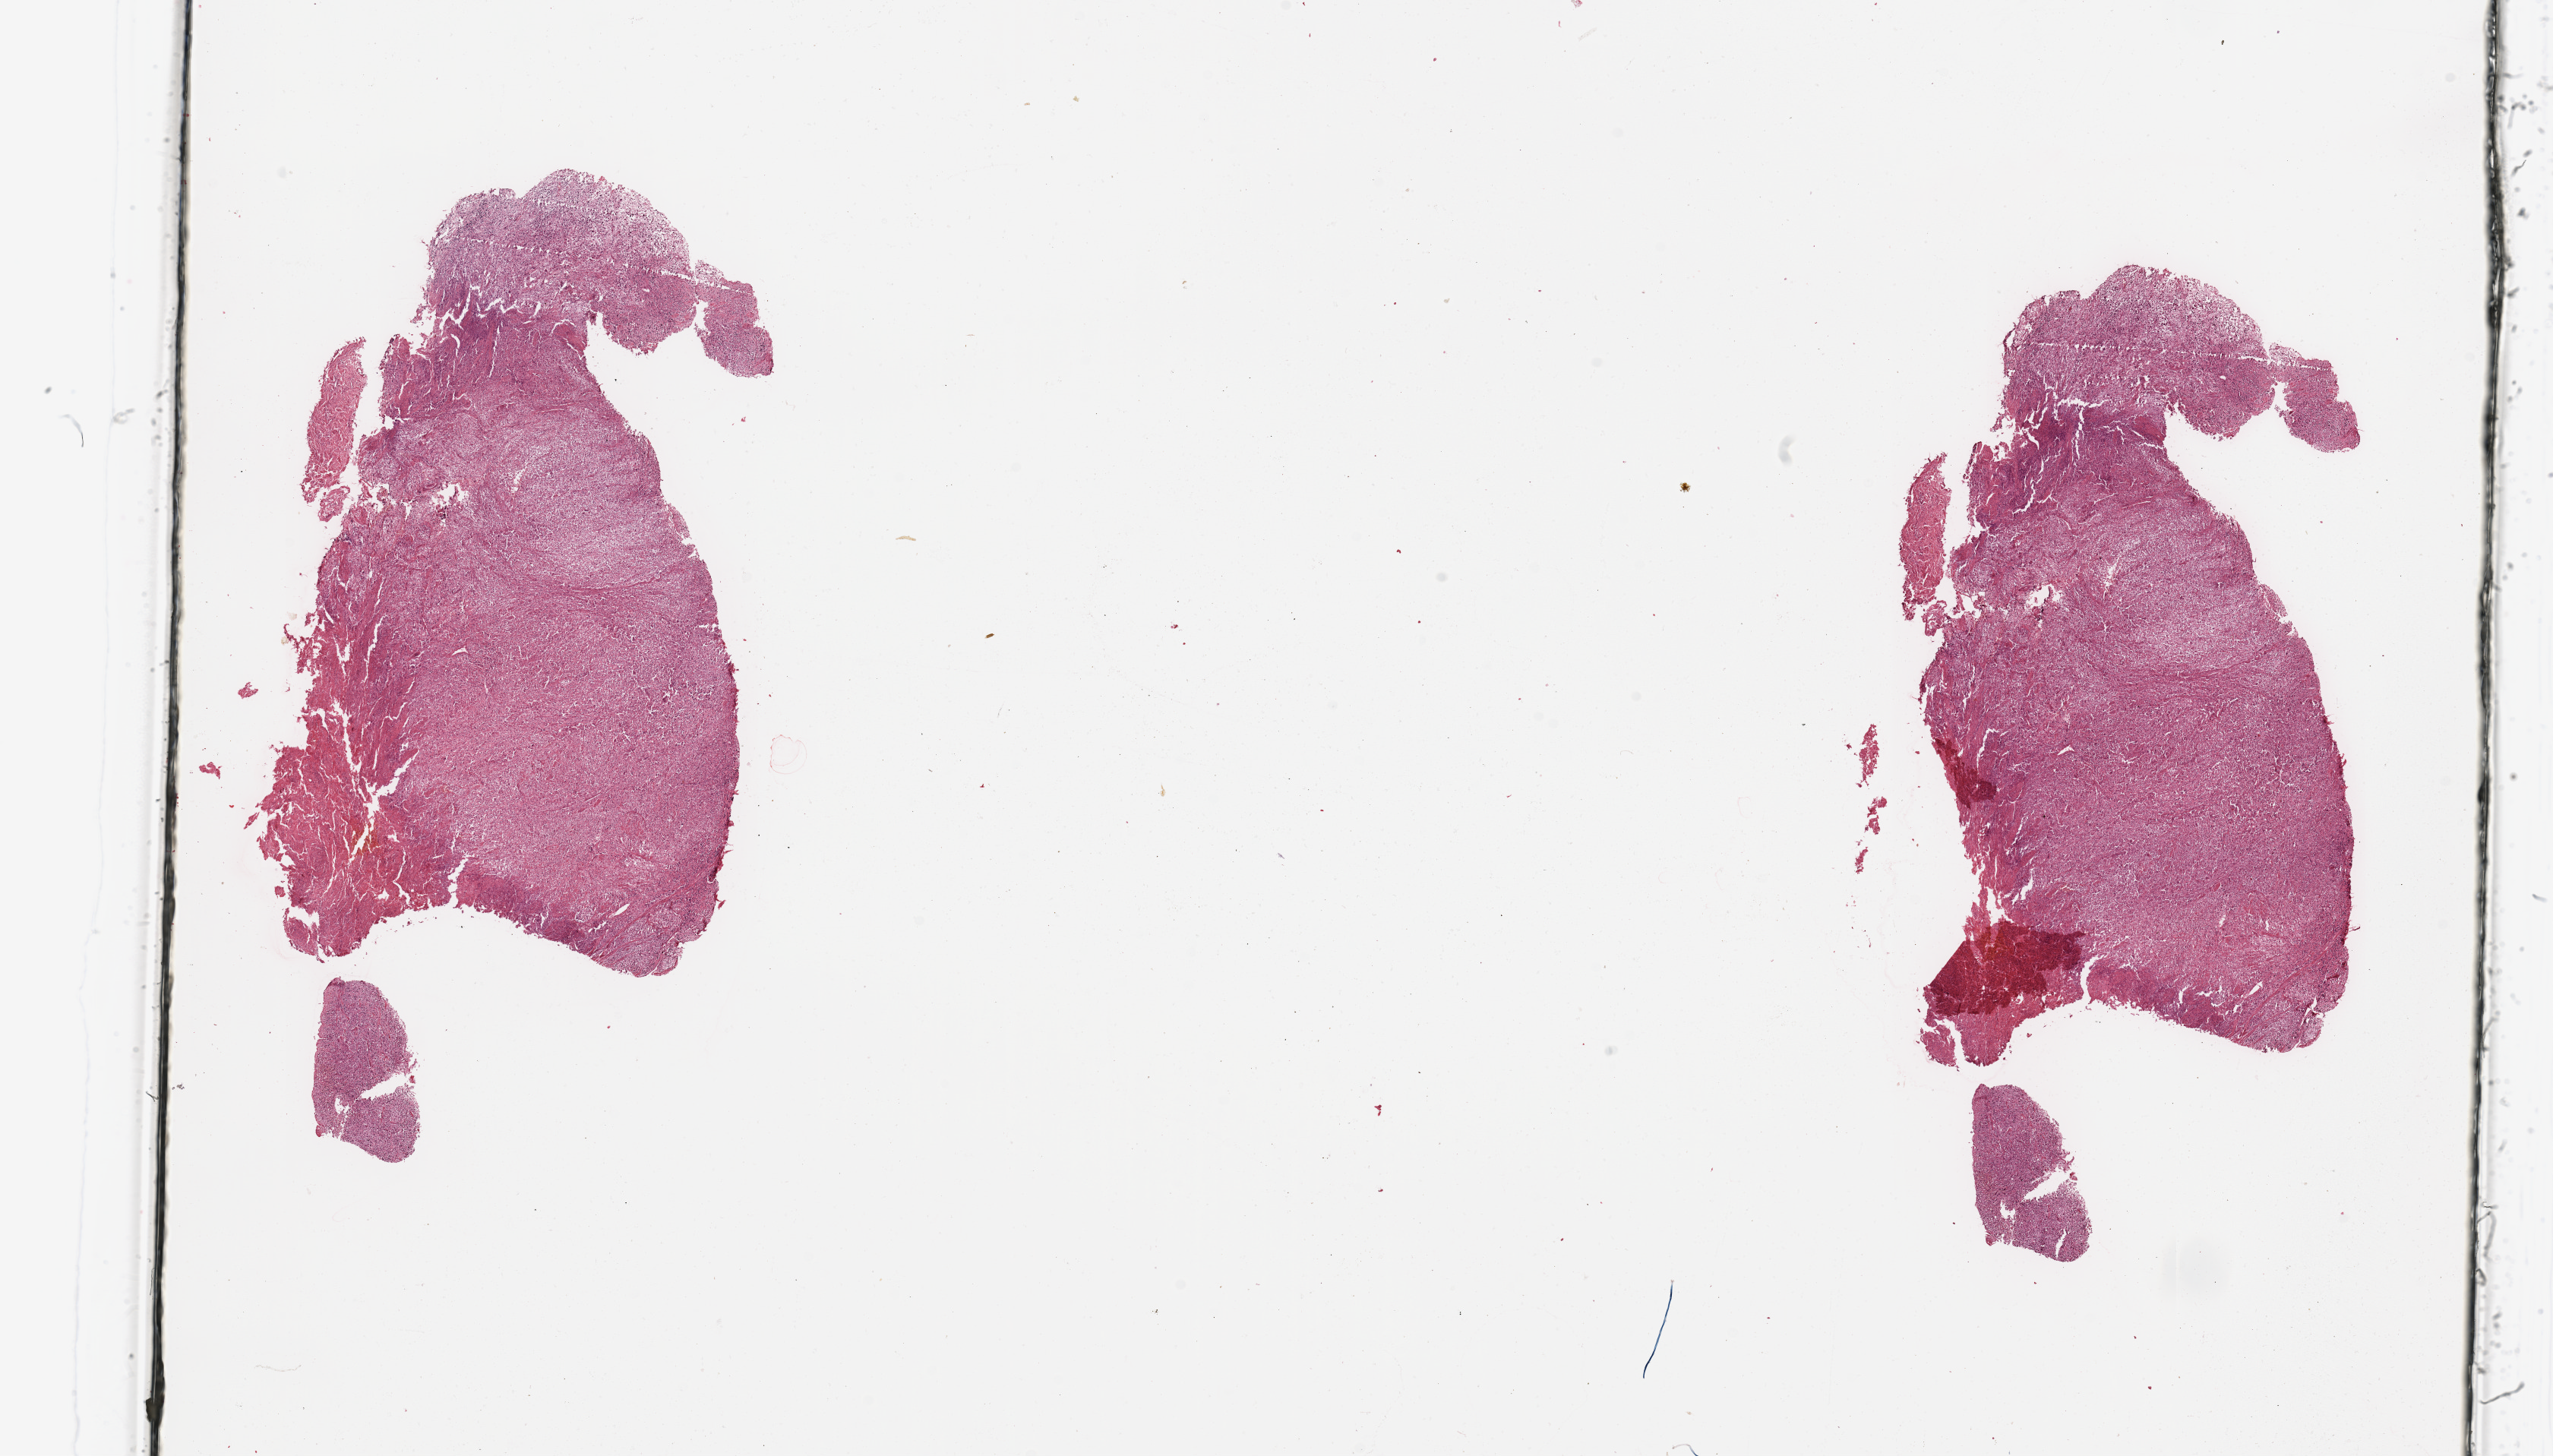
Digitized H&E tissue section (whole slide) — low-resolution overview of the scanned area, about 26.6 x 15.2 mm (acquisition: 20x scan). Patient: female, age 80 years.
Patient diagnosis (cohort enrolment): sarcoma (site not recorded at cohort level). Primary tumour site (as recorded): gynecologic.